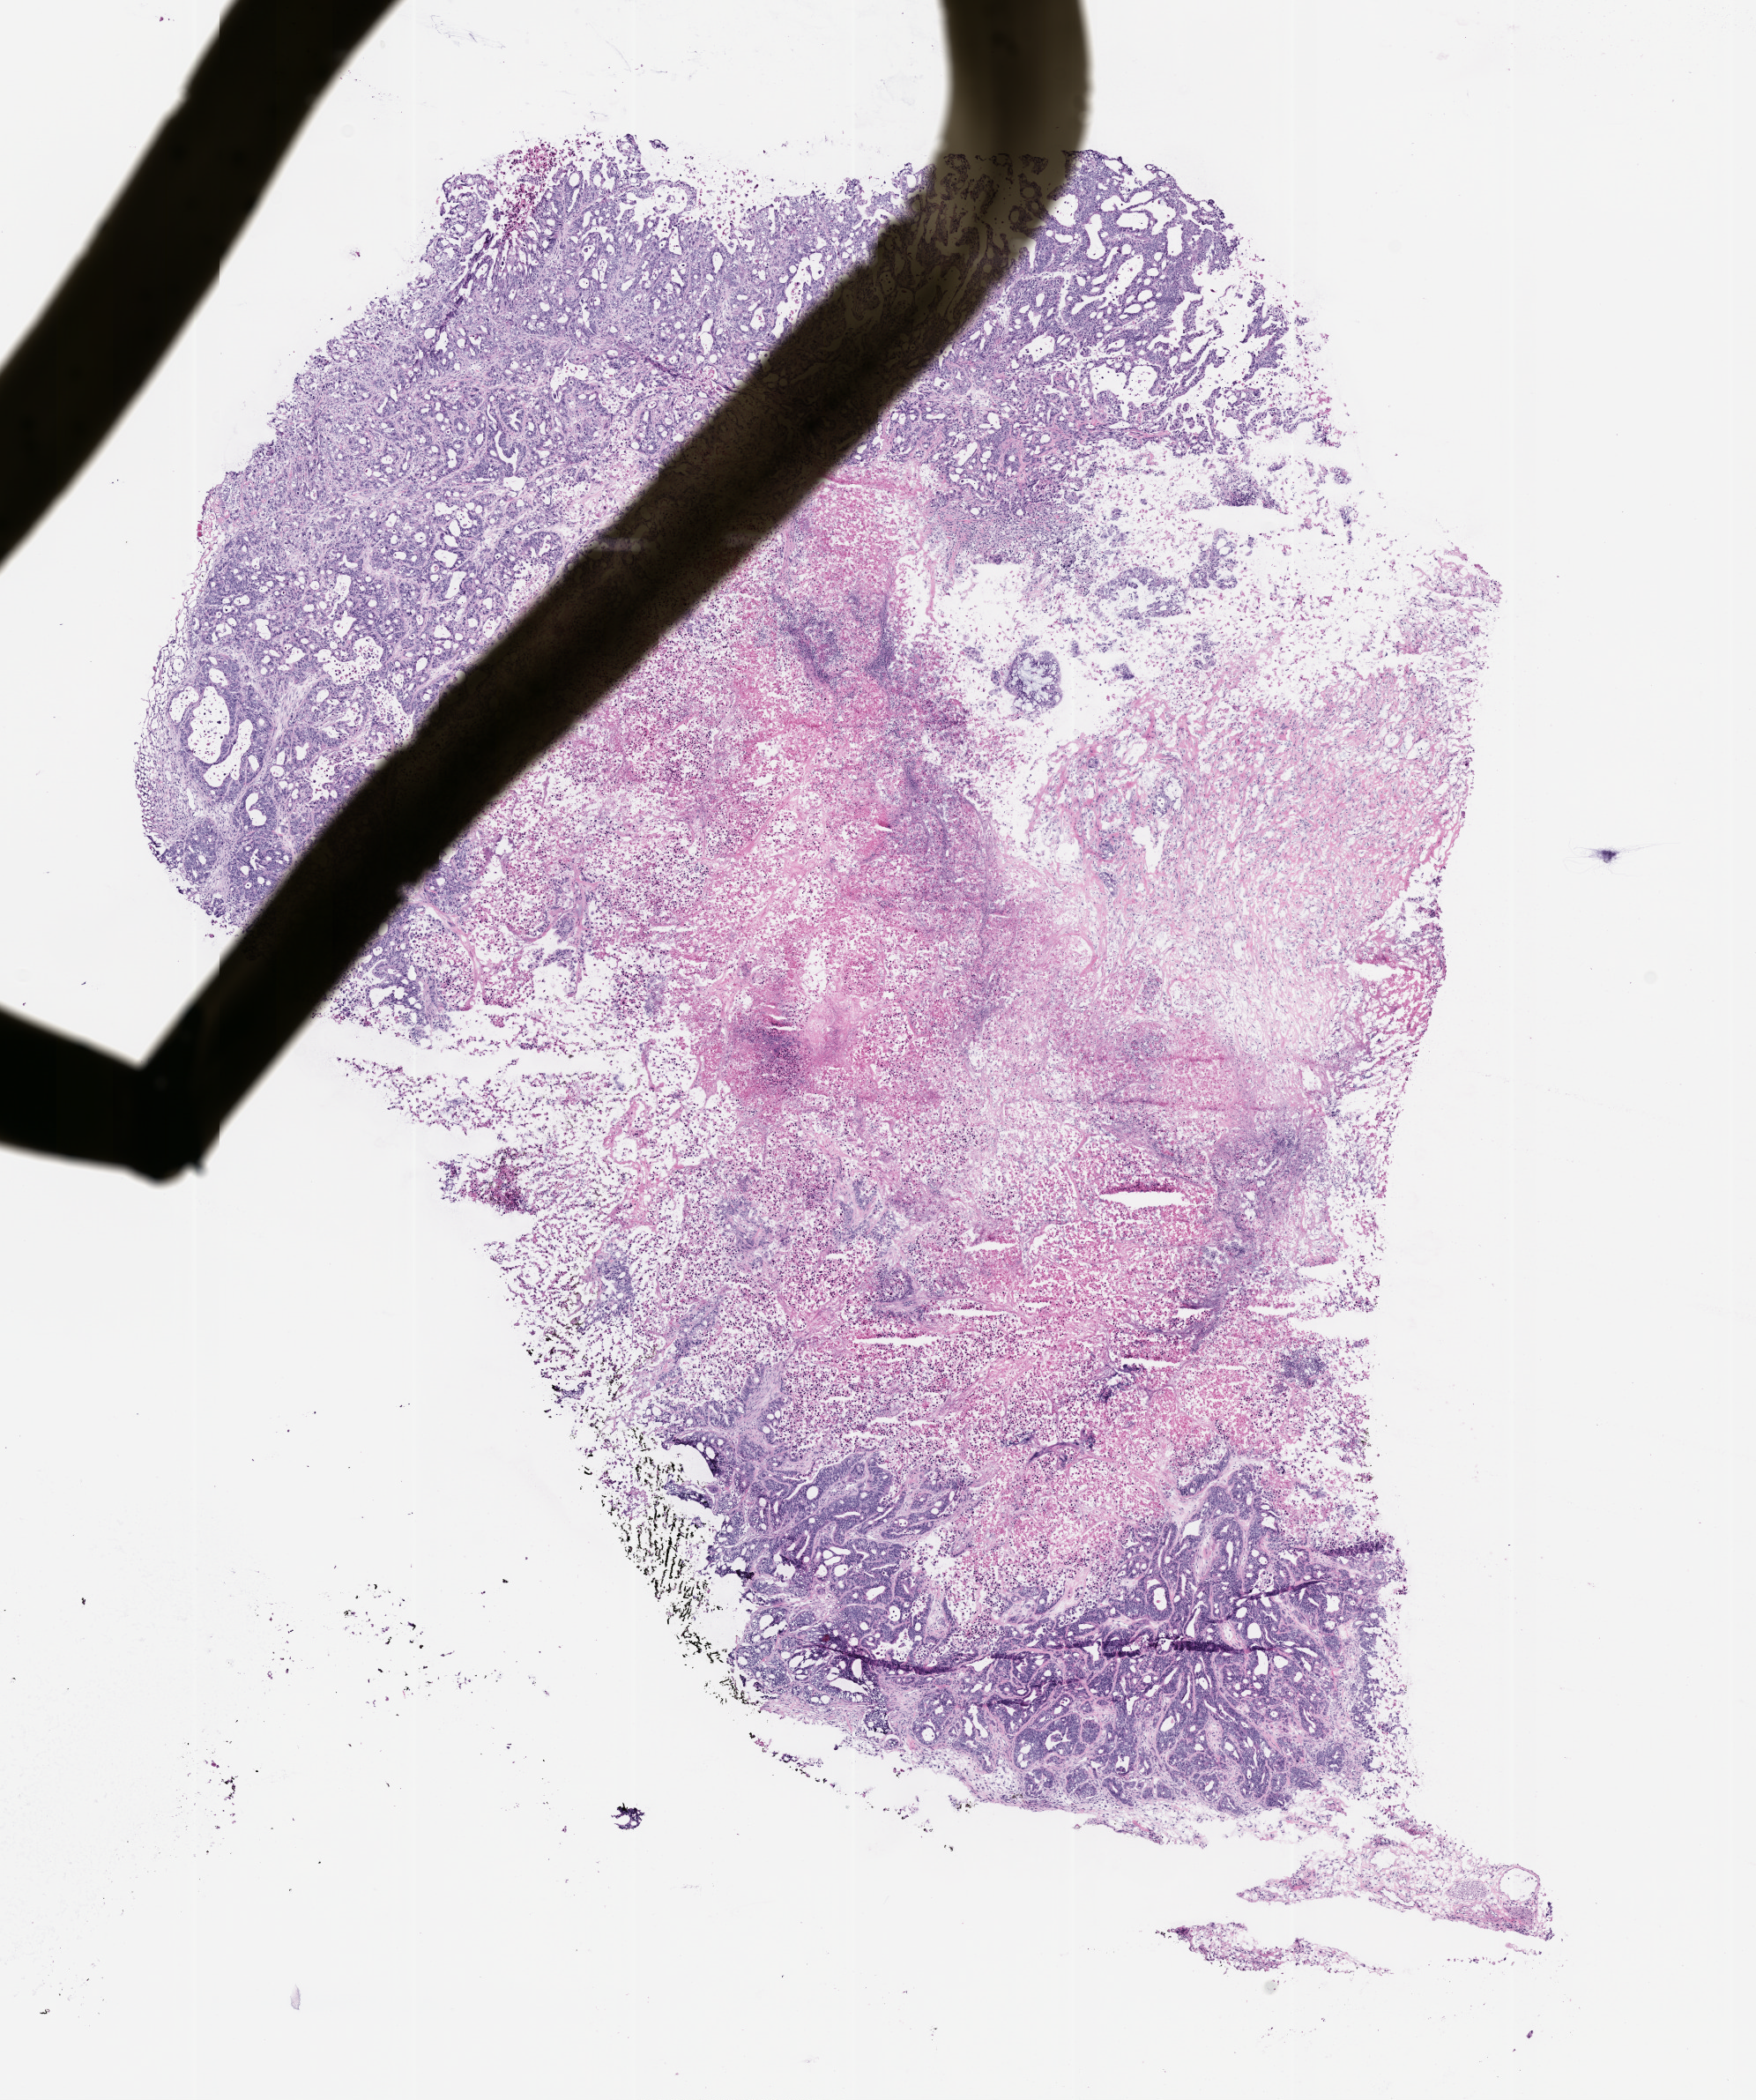
H&E whole-slide image of a patient-derived xenograft (PDX) tumor grown in a mouse, passage 0, whole scanned area (about 8.0 x 9.6 mm) shown as a low-resolution overview, formalin-fixed, paraffin-embedded (FFPE) tissue, tumor site category: pancreas.
Originating patient diagnosis: Pancreatic Adenocarcinoma.